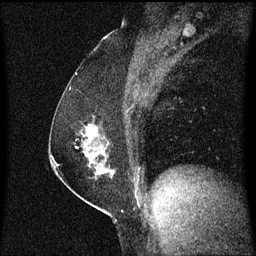
Breast MRI (dynamic contrast-enhanced), one sagittal slice; position 36 of 60 along the scan axis; dynamic contrast-enhanced series, image 2 of 3 at this slice position (ordered by acquisition); 1.5 T; TE 4.2 ms, TR 8.4 ms; 2 mm slice thickness; 256 × 256 image matrix. Patient: female, 52 years. From the clinical record (not read from this slice): setting: breast cancer imaged before/during neoadjuvant chemotherapy; receptor status: HER2-positive.
Structures marked on this image (semi-automatically segmented with operator editing):
- analysis volume of interest (the breast-tissue region the enhancement analysis was run in; not a lesion): bounding box <67,120,108,187> (left, top, right, bottom; pixels)
- tumour enhancement mask (voxels above the 70 % enhancement threshold inside the analysis volume of interest): <89,130,98,137>